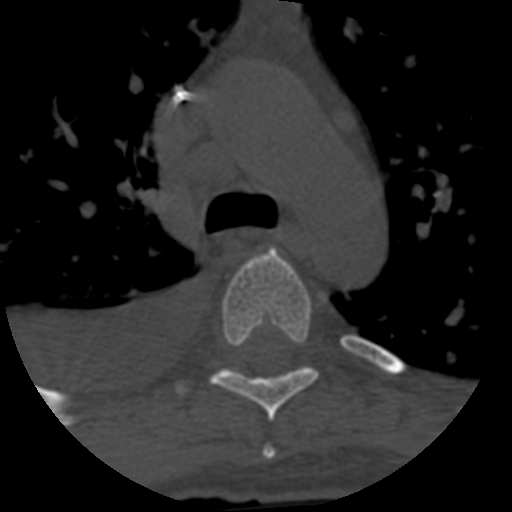
CT including the spine, one axial slice; position 453 of 708 along the scan axis; reconstruction kernel STANDARD; one of 3 acquisitions stored at this slice position; bone window (W 1800 / L 400 HU); 1.25 mm slice thickness; 512 × 512 image matrix, field of view 160 × 160 mm. Patient age 55 years. Case-level facts recorded for this patient, not image findings: primary cancer: colon.
Outlined on this slice (semi-automatic segmentation, software-assisted and operator-edited):
- T4 vertebra: bounding box [x1, y1, x2, y2] px = [262, 446, 276, 460]
- T5 vertebra: [211, 249, 318, 421]